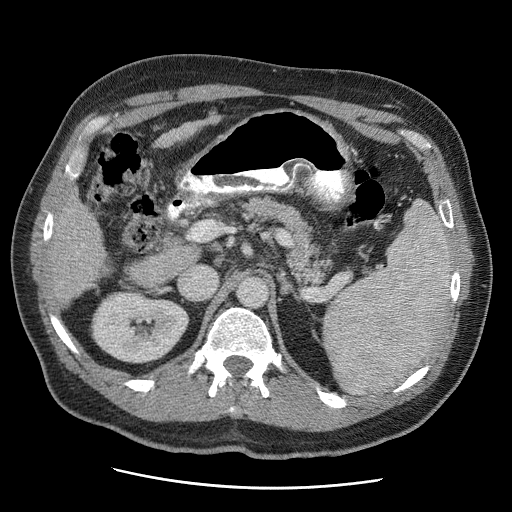
Contrast-enhanced abdominal CT (liver protocol), one axial slice. Position 19 of 81 along the scan axis. Reconstruction kernel STANDARD. Soft-tissue window (W 400 / L 40 HU). 2.5 mm slice thickness. 512 × 512 image matrix, field of view 380 × 380 mm. Case-level facts recorded for this patient, not image findings: diagnosis: hepatocellular carcinoma (patient treated with transarterial chemoembolisation; whether this scan precedes or follows treatment is not stated here); TNM stage (as recorded): Stage-IIIA; Child-Pugh class: A; tumour differentiation: moderately differentiated; tumour nodularity: multinodular.
Annotated regions visible in this slice (semi-automatically segmented with operator editing):
- liver parenchyma outside the tumour (the mass and vessels are separate outlines, so this box may not span the whole liver): bounding box (x1, y1, x2, y2) in pixels: (48, 116, 217, 304)